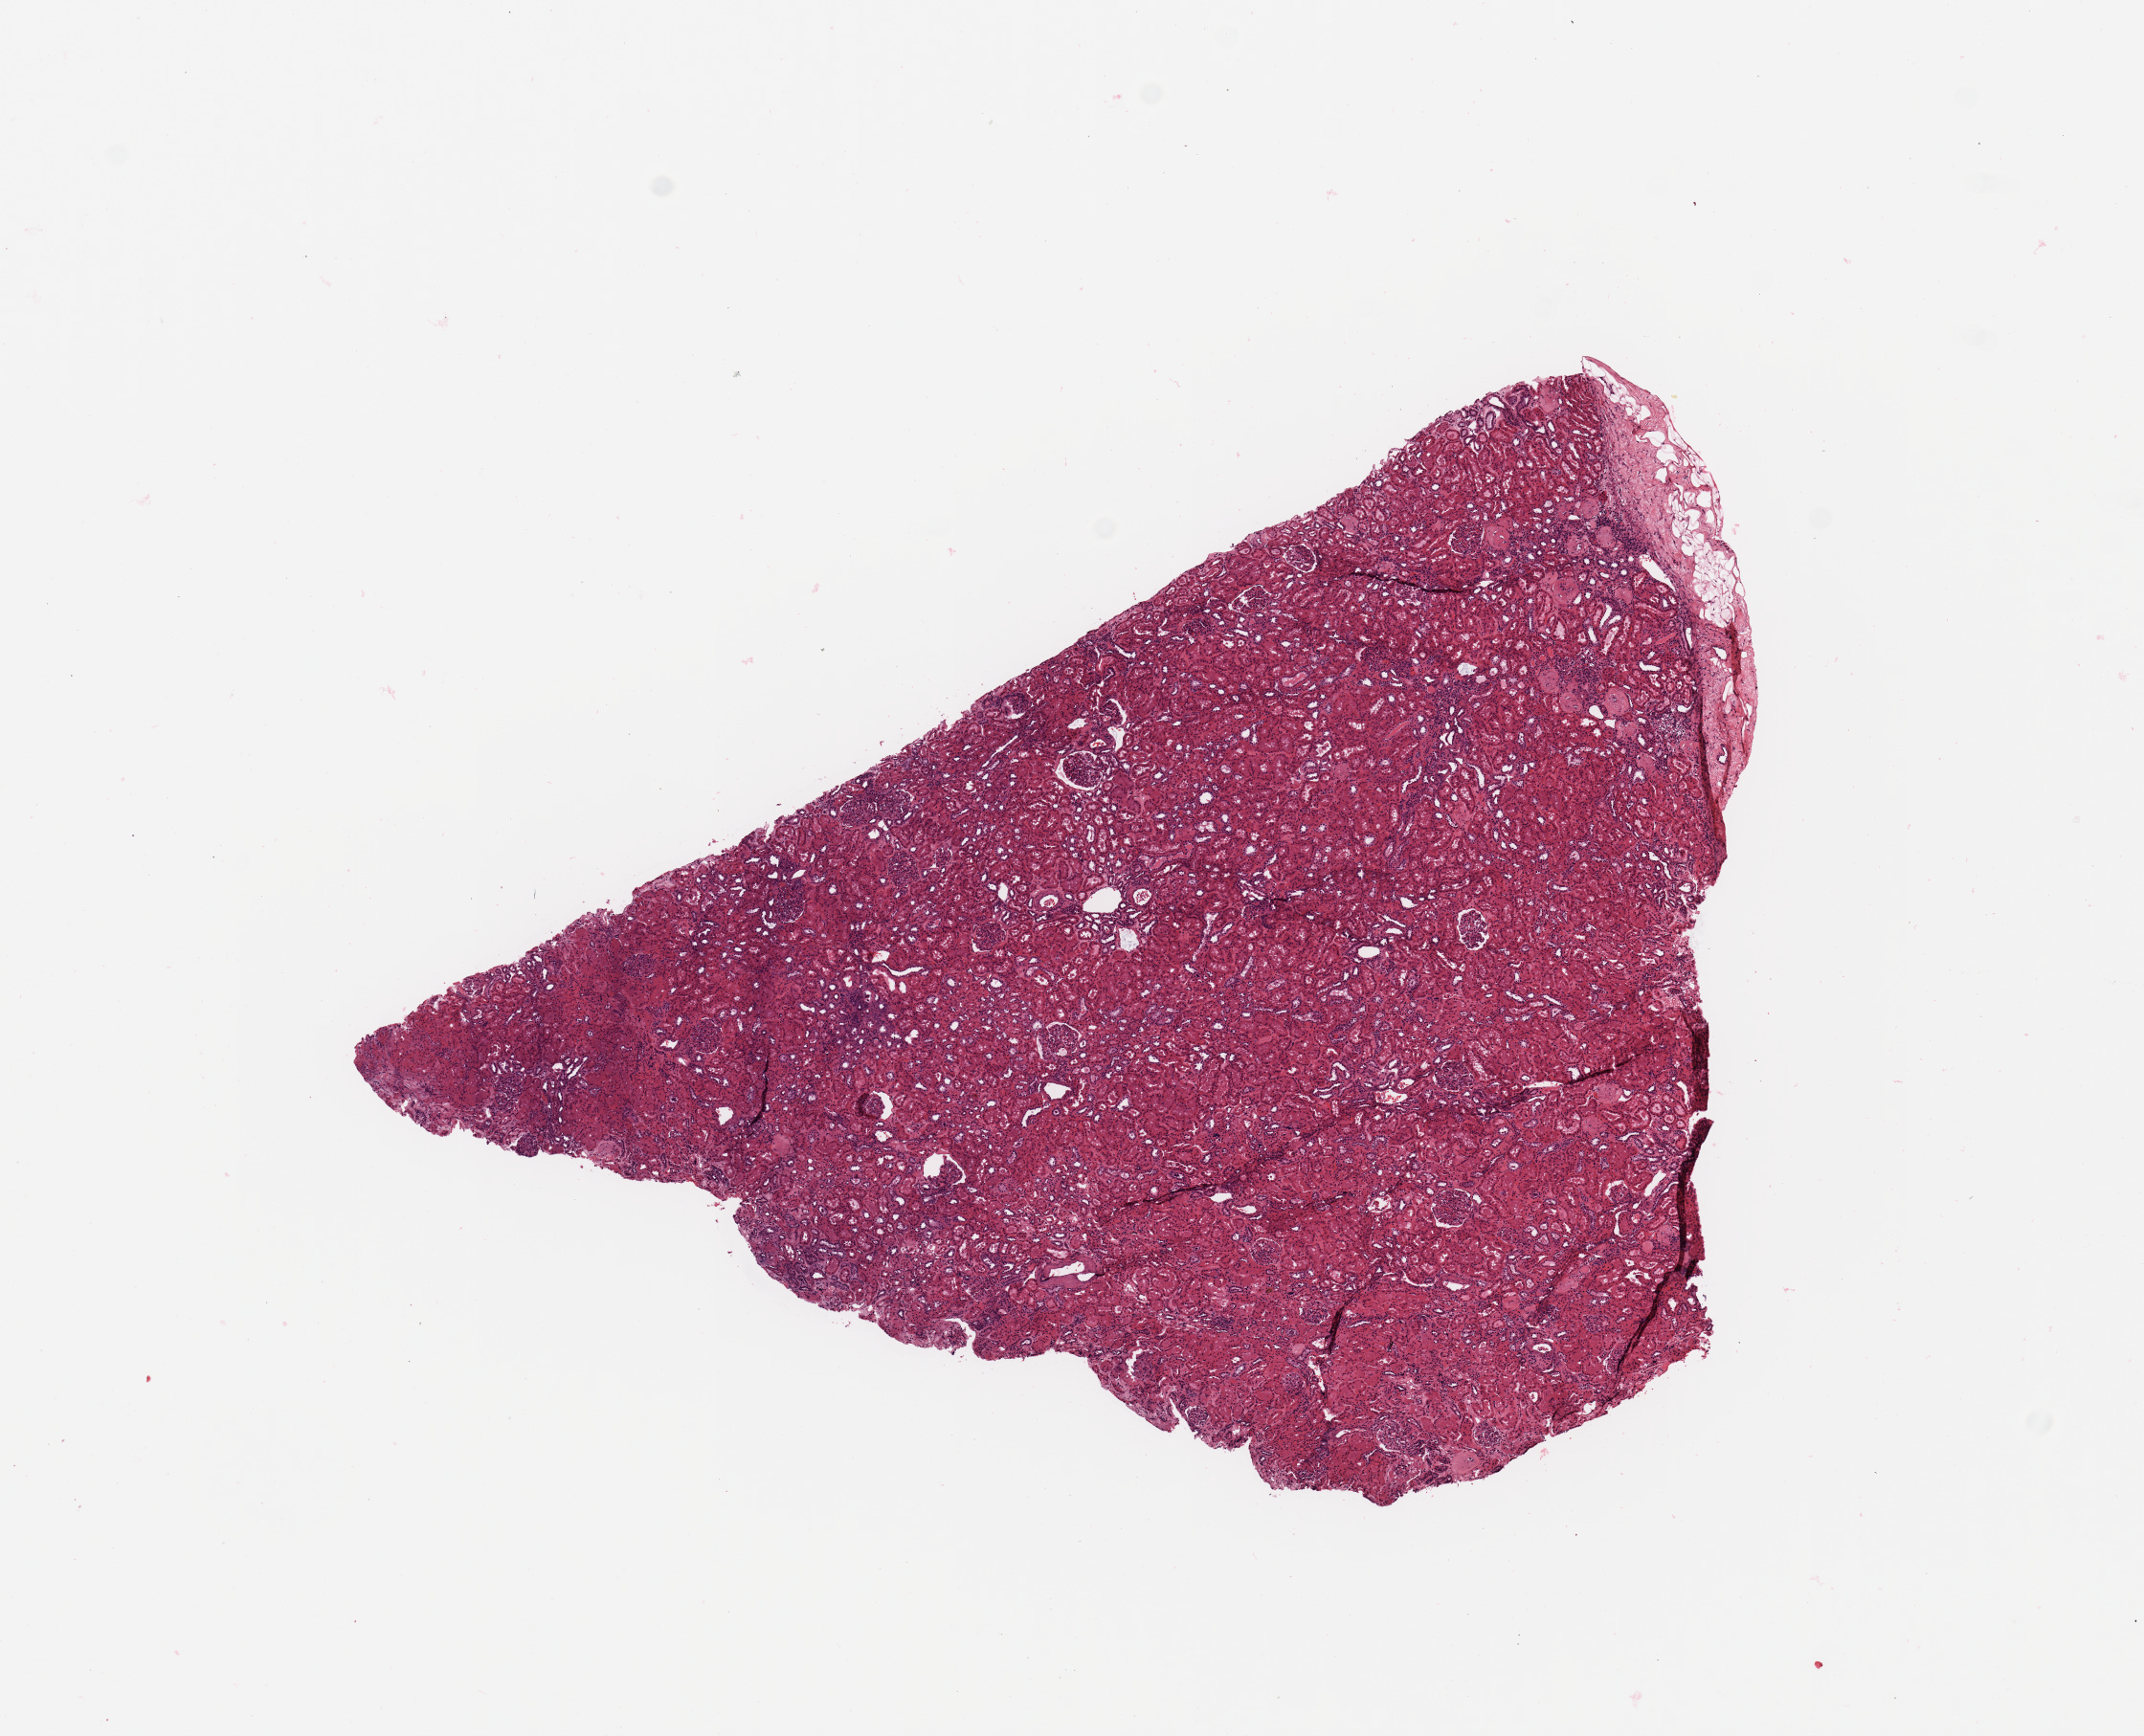
Whole-slide histology image, H&E — a low-resolution overview of the entire scanned area, about 8.9 x 7.2 mm (slide scanned at 20x). Normal (non-tumour) tissue sample, kidney. 64-year-old female patient.
This section: normal (non-tumour) tissue from the same patient. Patient diagnosis: Renal cell carcinoma, NOS.